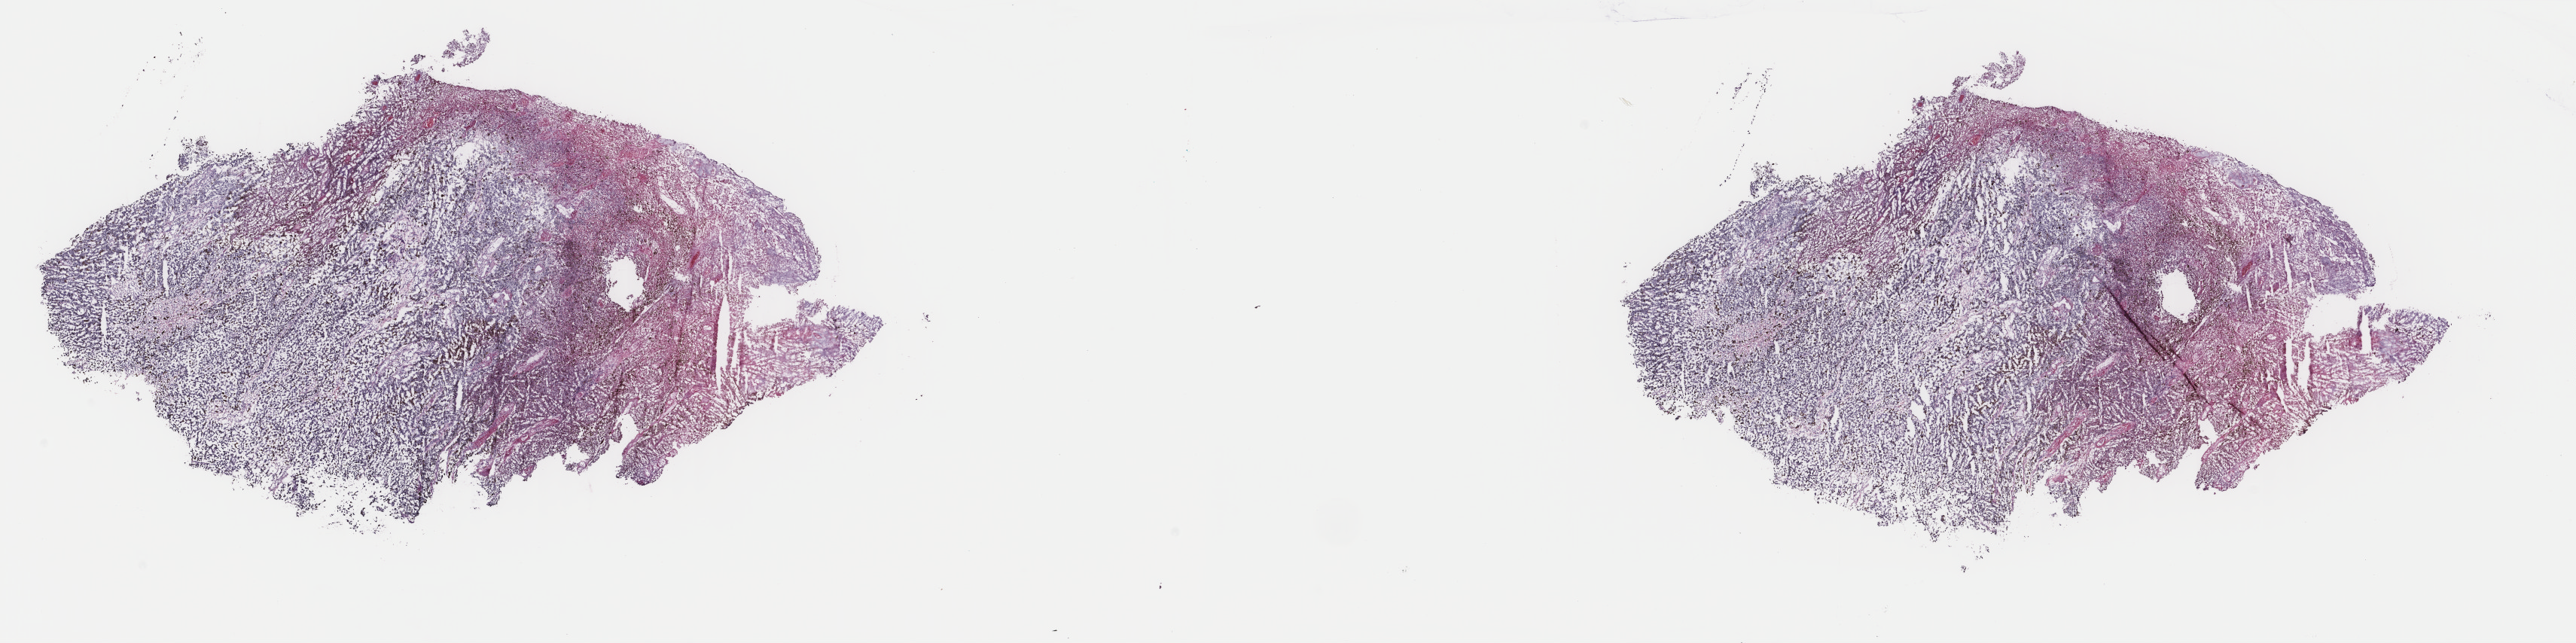
Whole-slide histology image, Hematoxylin and eosin (H&E) stained, whole scanned area (about 27.2 x 6.8 mm, from a 40x scan) shown as a low-resolution overview, frozen section from the top of the tissue portion, metastatic tumour sample, sampled site not recorded. Female patient. Composition of this section per pathologist review: tumour cells 75%, tumour nuclei 90%, normal cells 0%, stromal cells 5%, necrosis 20%. Infiltration values recorded for this section: lymphocyte infiltration 0%, monocyte infiltration 0%, neutrophil infiltration 0%.
* this section: metastatic tumour tissue
* patient diagnosis: Malignant melanoma, NOS